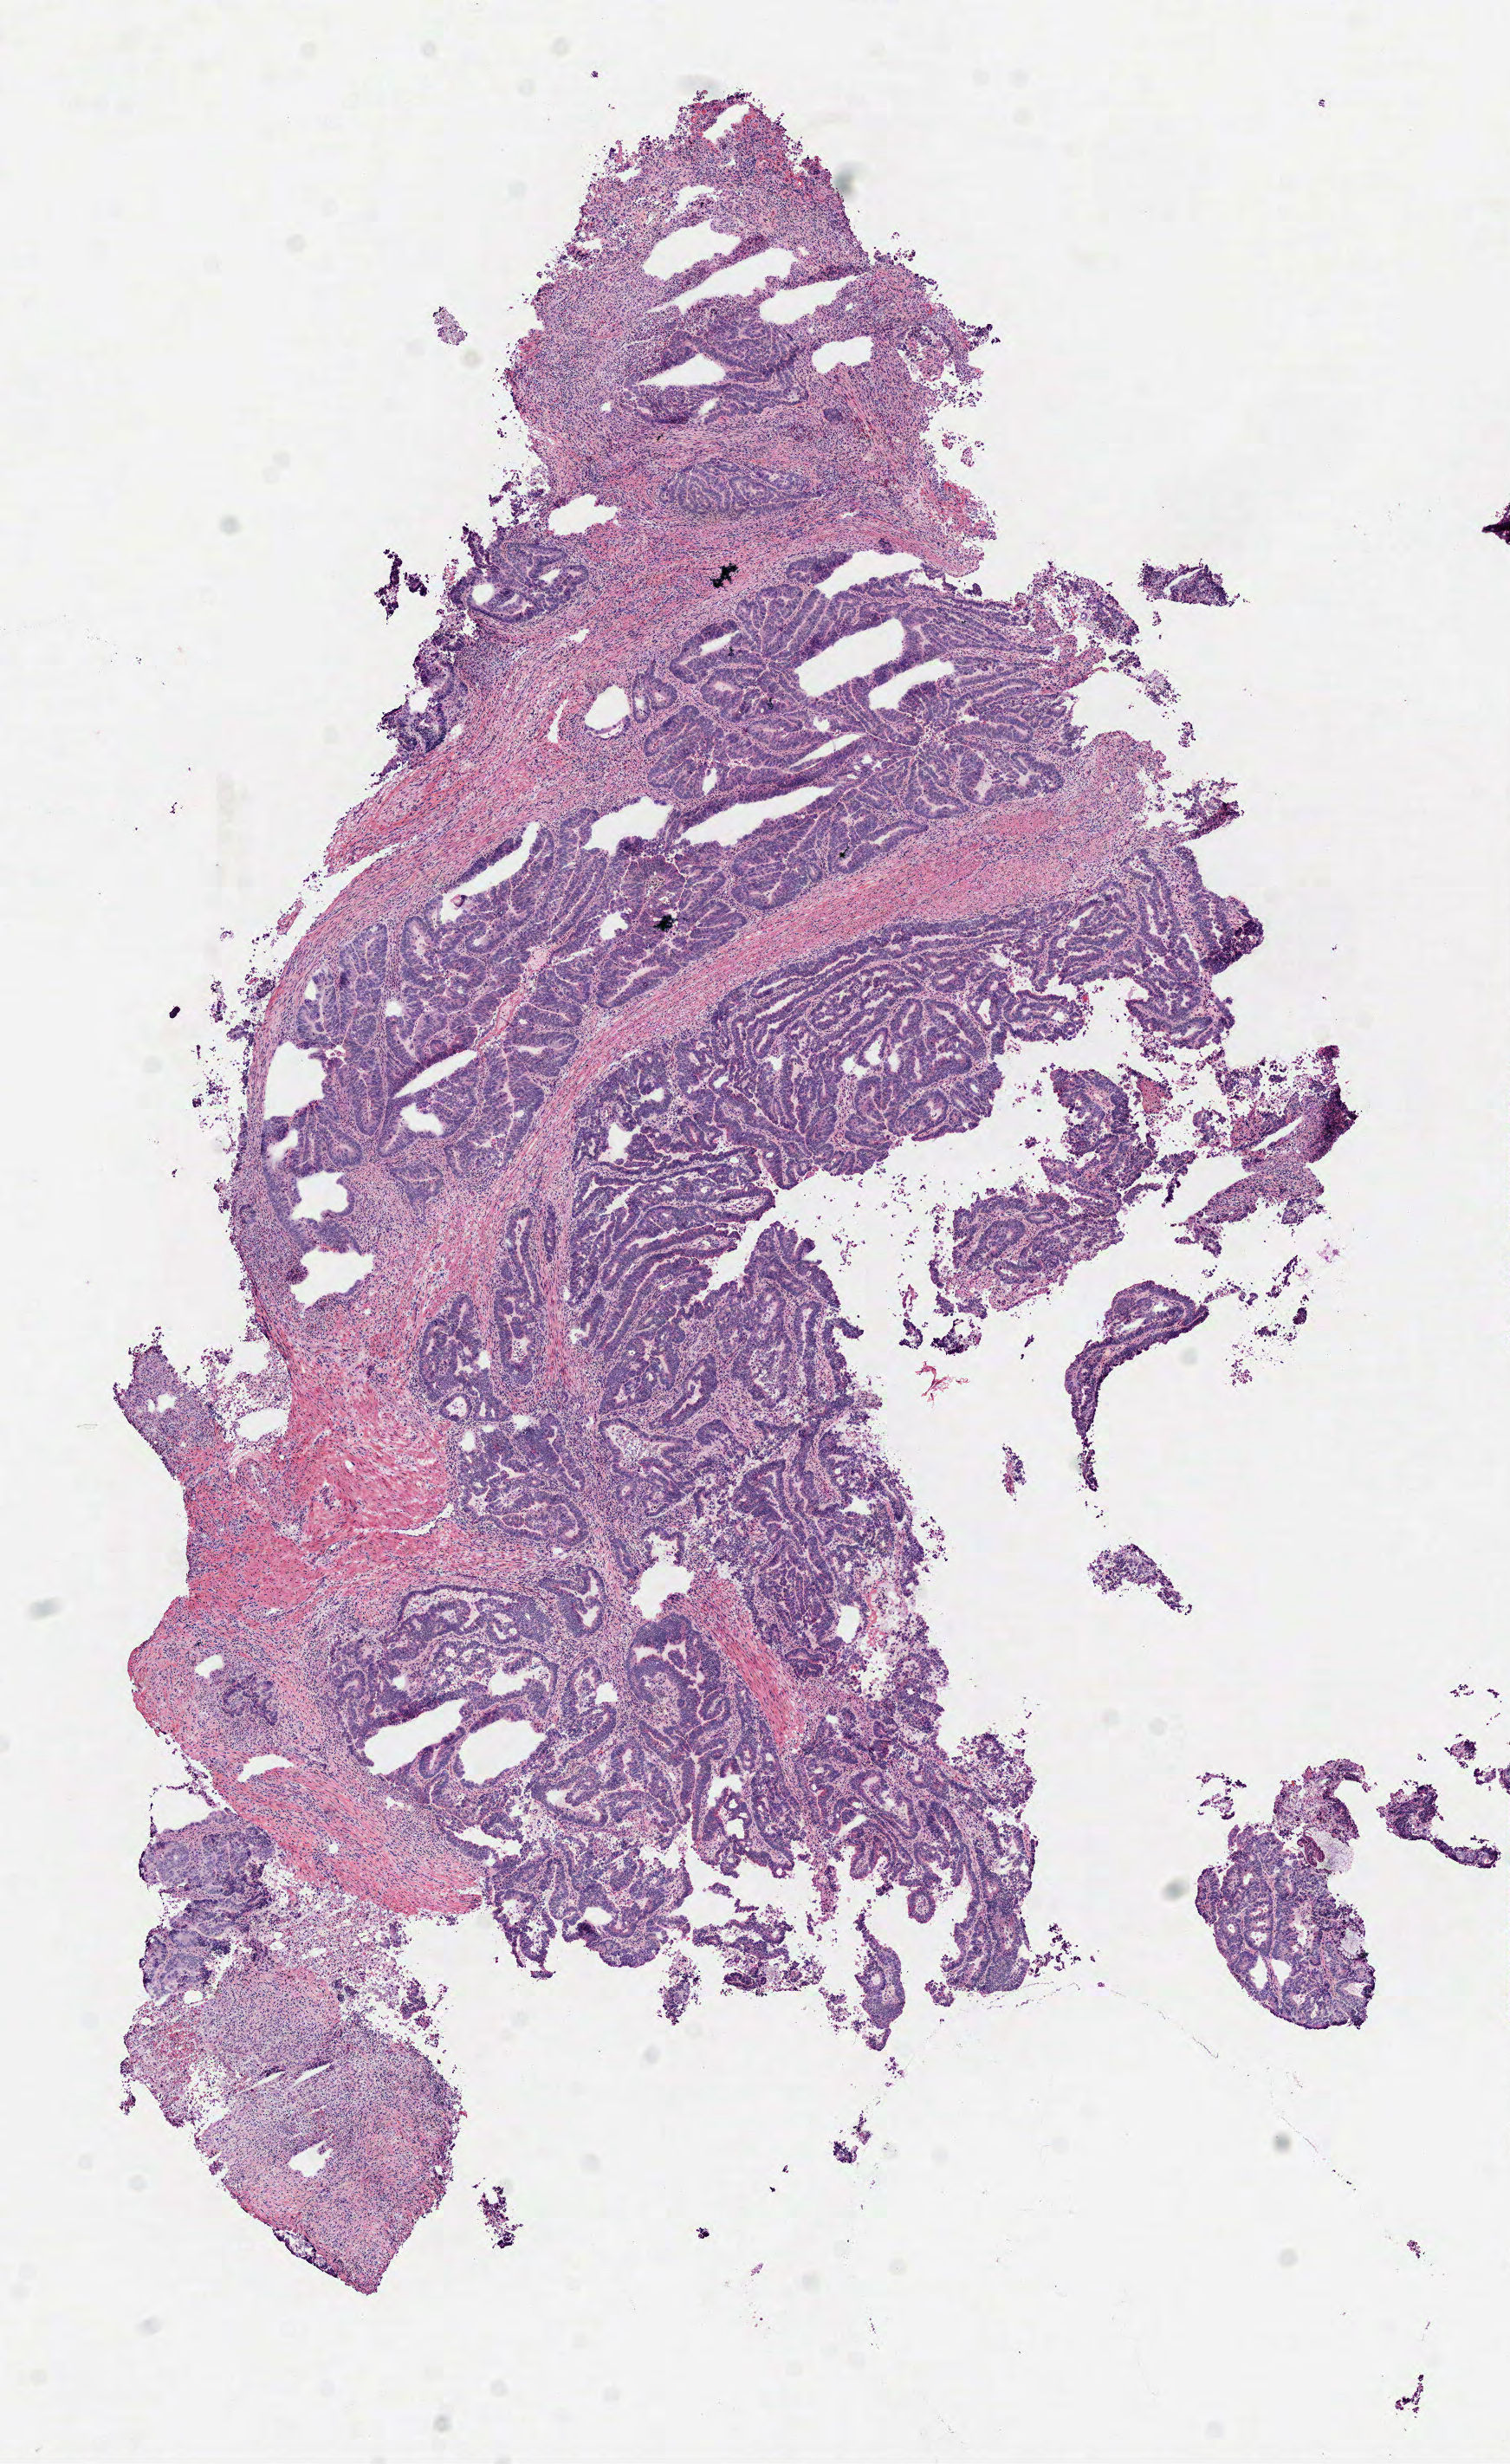
H&E-stained whole-slide image — shown as a low-resolution overview of the whole scanned area (about 7.0 x 11.5 mm). Frozen section from the top of the tissue portion. Sample: primary tumour, rectum. Male patient; age at initial diagnosis 57 years. Pathologist review of this section (percent, as recorded): tumour cells 72%, tumour nuclei 75%, normal cells 0%, stromal cells 25%, necrosis 3%.
- lymph nodes positive (case pathology): 0 of 24 examined
- histologic diagnosis: Adenocarcinoma, NOS
- AJCC pathologic stage: IIA